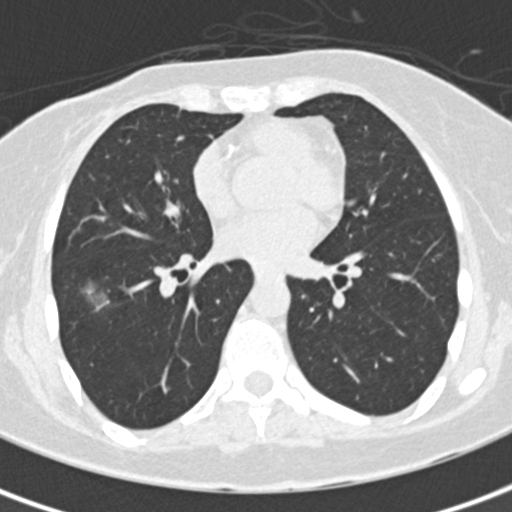
Axial slice from a low-dose chest CT screening exam; baseline annual screen; lung window (W 1500 / L -600 HU); 2 mm slice thickness; 120 kVp; 512 × 512 image matrix, field of view 284 × 284 mm. Female participant, aged 56 years at enrolment.
Expert-annotated lung lesion, box from (x=74, y=274) to (x=132, y=329) px. The screening reader recorded 5 non-calcified nodules or masses ≥4 mm on this exam; which of them this box marks is not recorded. Lung cancer was diagnosed 26 days after this screen: bronchiolo-alveolar carcinoma, mucinous, right lower lobe, well differentiated (G1), stage IA (AJCC 6th edition), 19 mm at pathology.